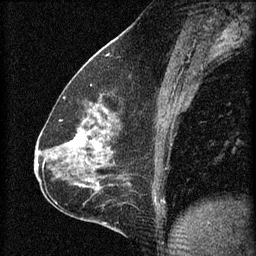
Breast MRI (dynamic contrast-enhanced), one sagittal slice; position 32 of 60 along the scan axis; 3 images stored at this slice position (order not interpretable as contrast timing); 1.5 T; TE 4.2 ms, TR 8.2 ms; 256 × 256 image matrix, field of view 180 × 180 mm. Female patient, age 59 years.
Structures marked on this image (semi-automatically segmented with operator editing):
- analysis volume of interest (the breast-tissue region the enhancement analysis was run in; not a lesion): bounding box [x1, y1, x2, y2] px = [61, 104, 123, 161]
- tumour enhancement mask (voxels above the 70 % enhancement threshold inside the analysis volume of interest): [71, 110, 108, 151]